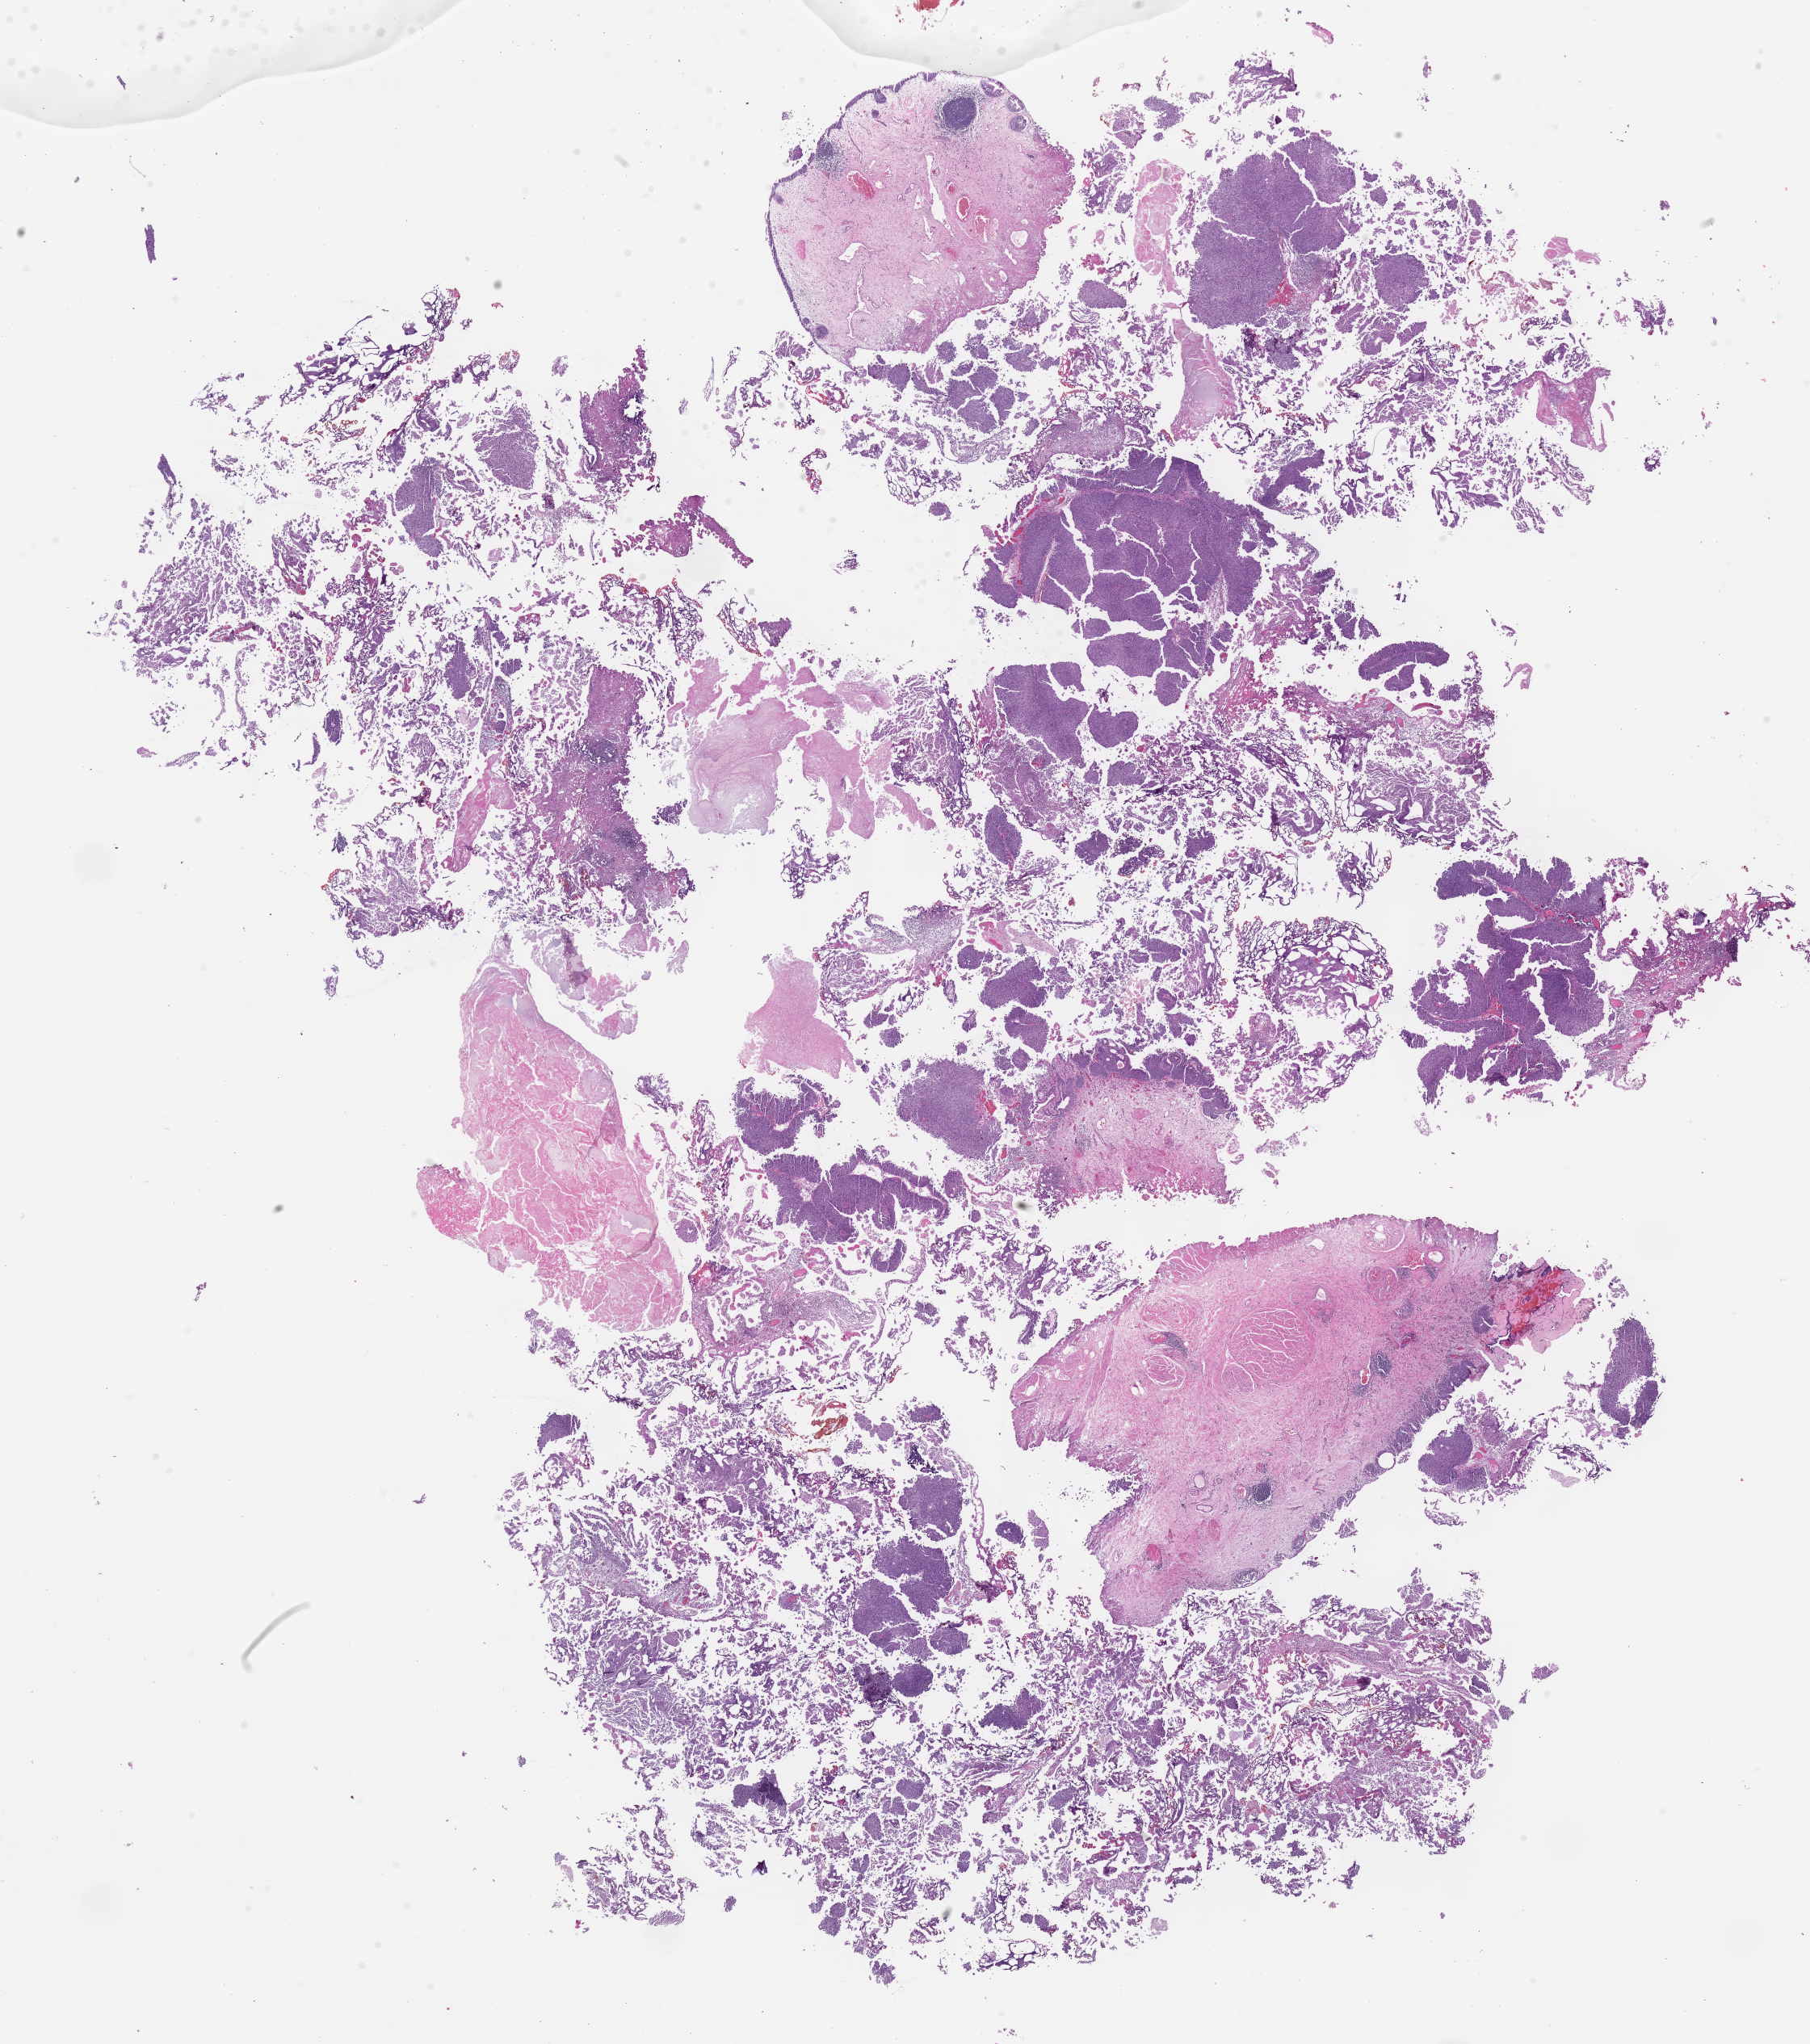
Whole-slide image, haematoxylin and eosin stain, whole scanned area (about 18.1 x 20.4 mm) shown as a low-resolution overview. FFPE section. Specimen: primary tumor. Site: bladder. Female, age 82 years at initial diagnosis. Slide review estimates, as recorded: tumor cells 40%, tumor nuclei 70%, stromal cells 60%, necrosis 0%, normal cells 0%. Inflammatory infiltration, as recorded: lymphocyte infiltration 0%, monocyte infiltration 0%, neutrophil infiltration 0%.
- histologic diagnosis: Papillary urothelial carcinoma, non-invasive